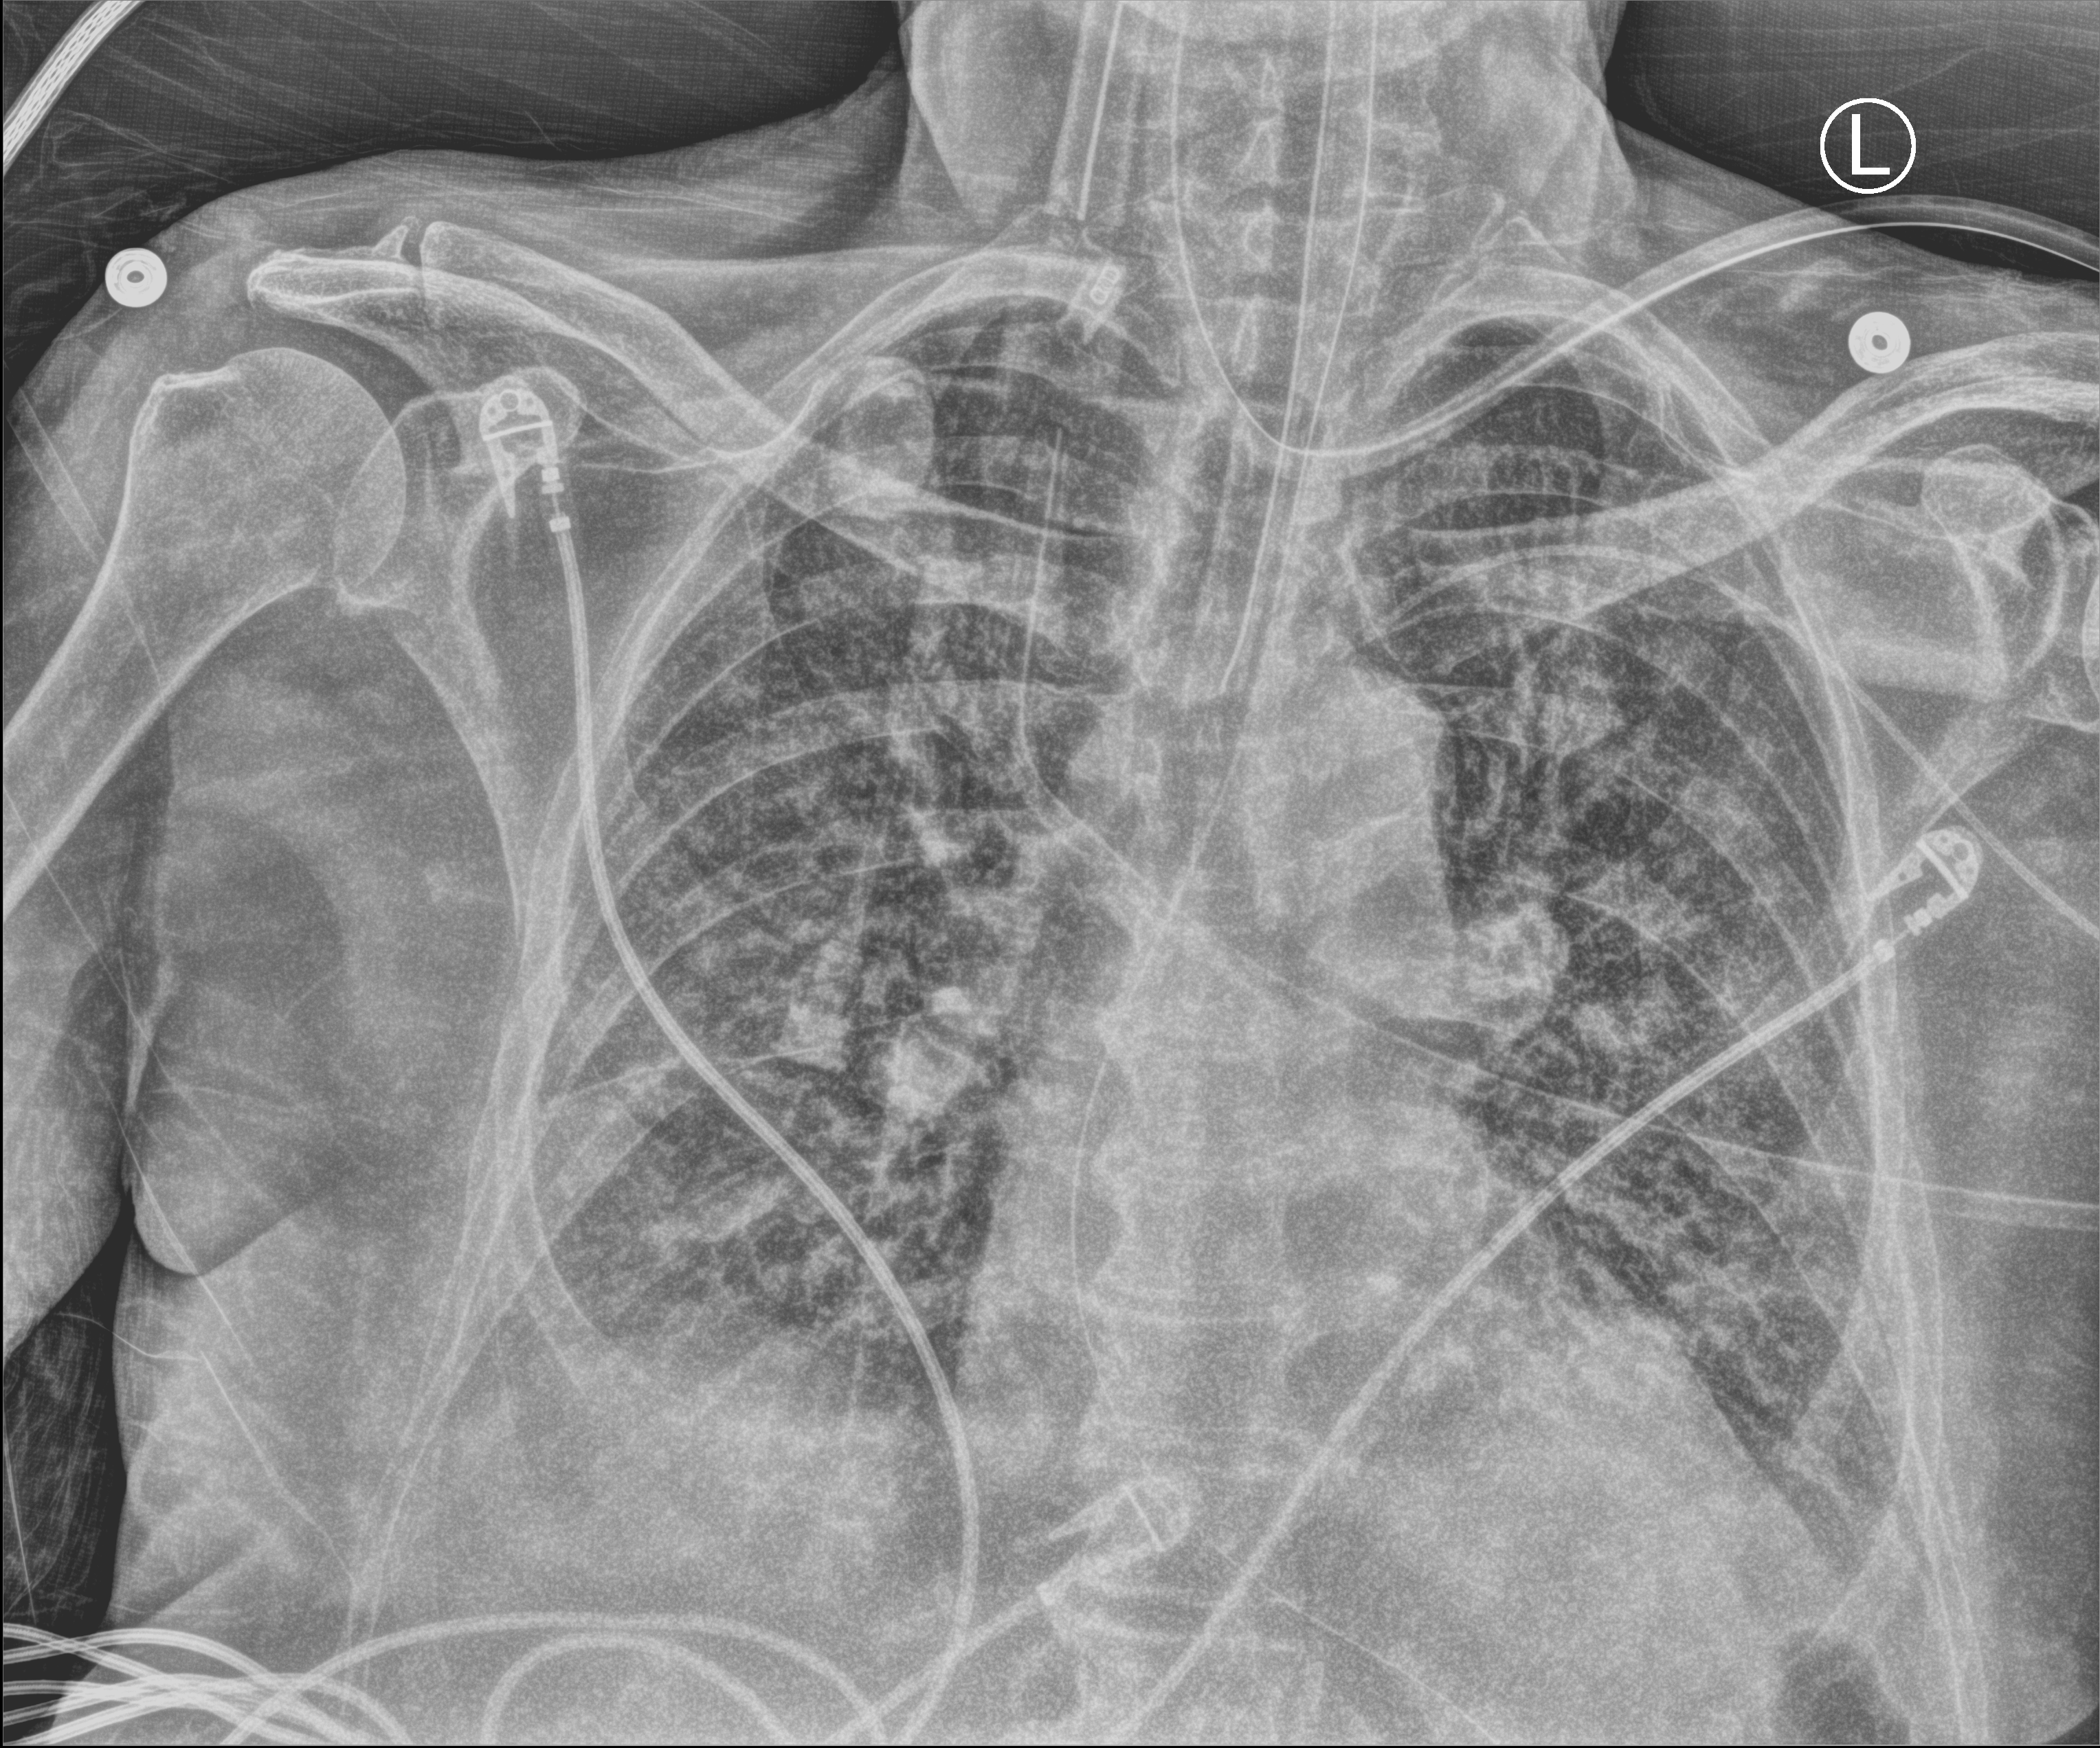
Bedside chest radiograph (computed radiography). Male patient hospitalised with COVID-19, age 75–90 years.
From the hospital-stay record, not from the radiograph (when in the stay this image was taken is not recorded): diabetes (admission record): no; smoking status (admission record): never.